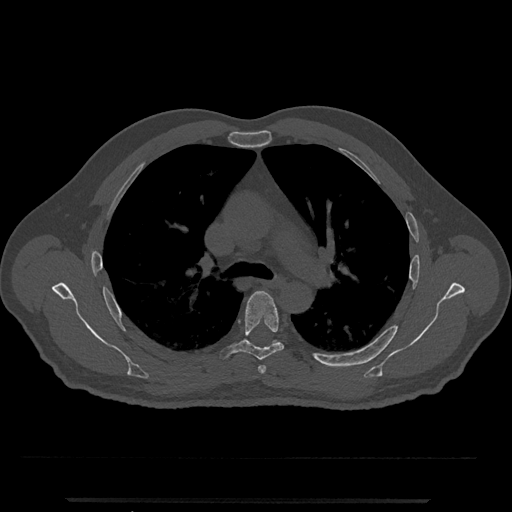
CT including the spine, one axial slice; slice 792 of 797 in the series (ordered by position); reconstruction kernel Br40s/3; bone window (W 1800 / L 400 HU); 0.5 mm slice thickness; 512 × 512 image matrix. Male patient, age 63 years. From the clinical record (not read from this slice): primary cancer: prostate.
Structures marked on this image (semi-automatically segmented with operator editing):
- T5 vertebra: bounding box [x1, y1, x2, y2] px = [220, 291, 284, 361]
- T6 vertebra: [272, 340, 280, 344]